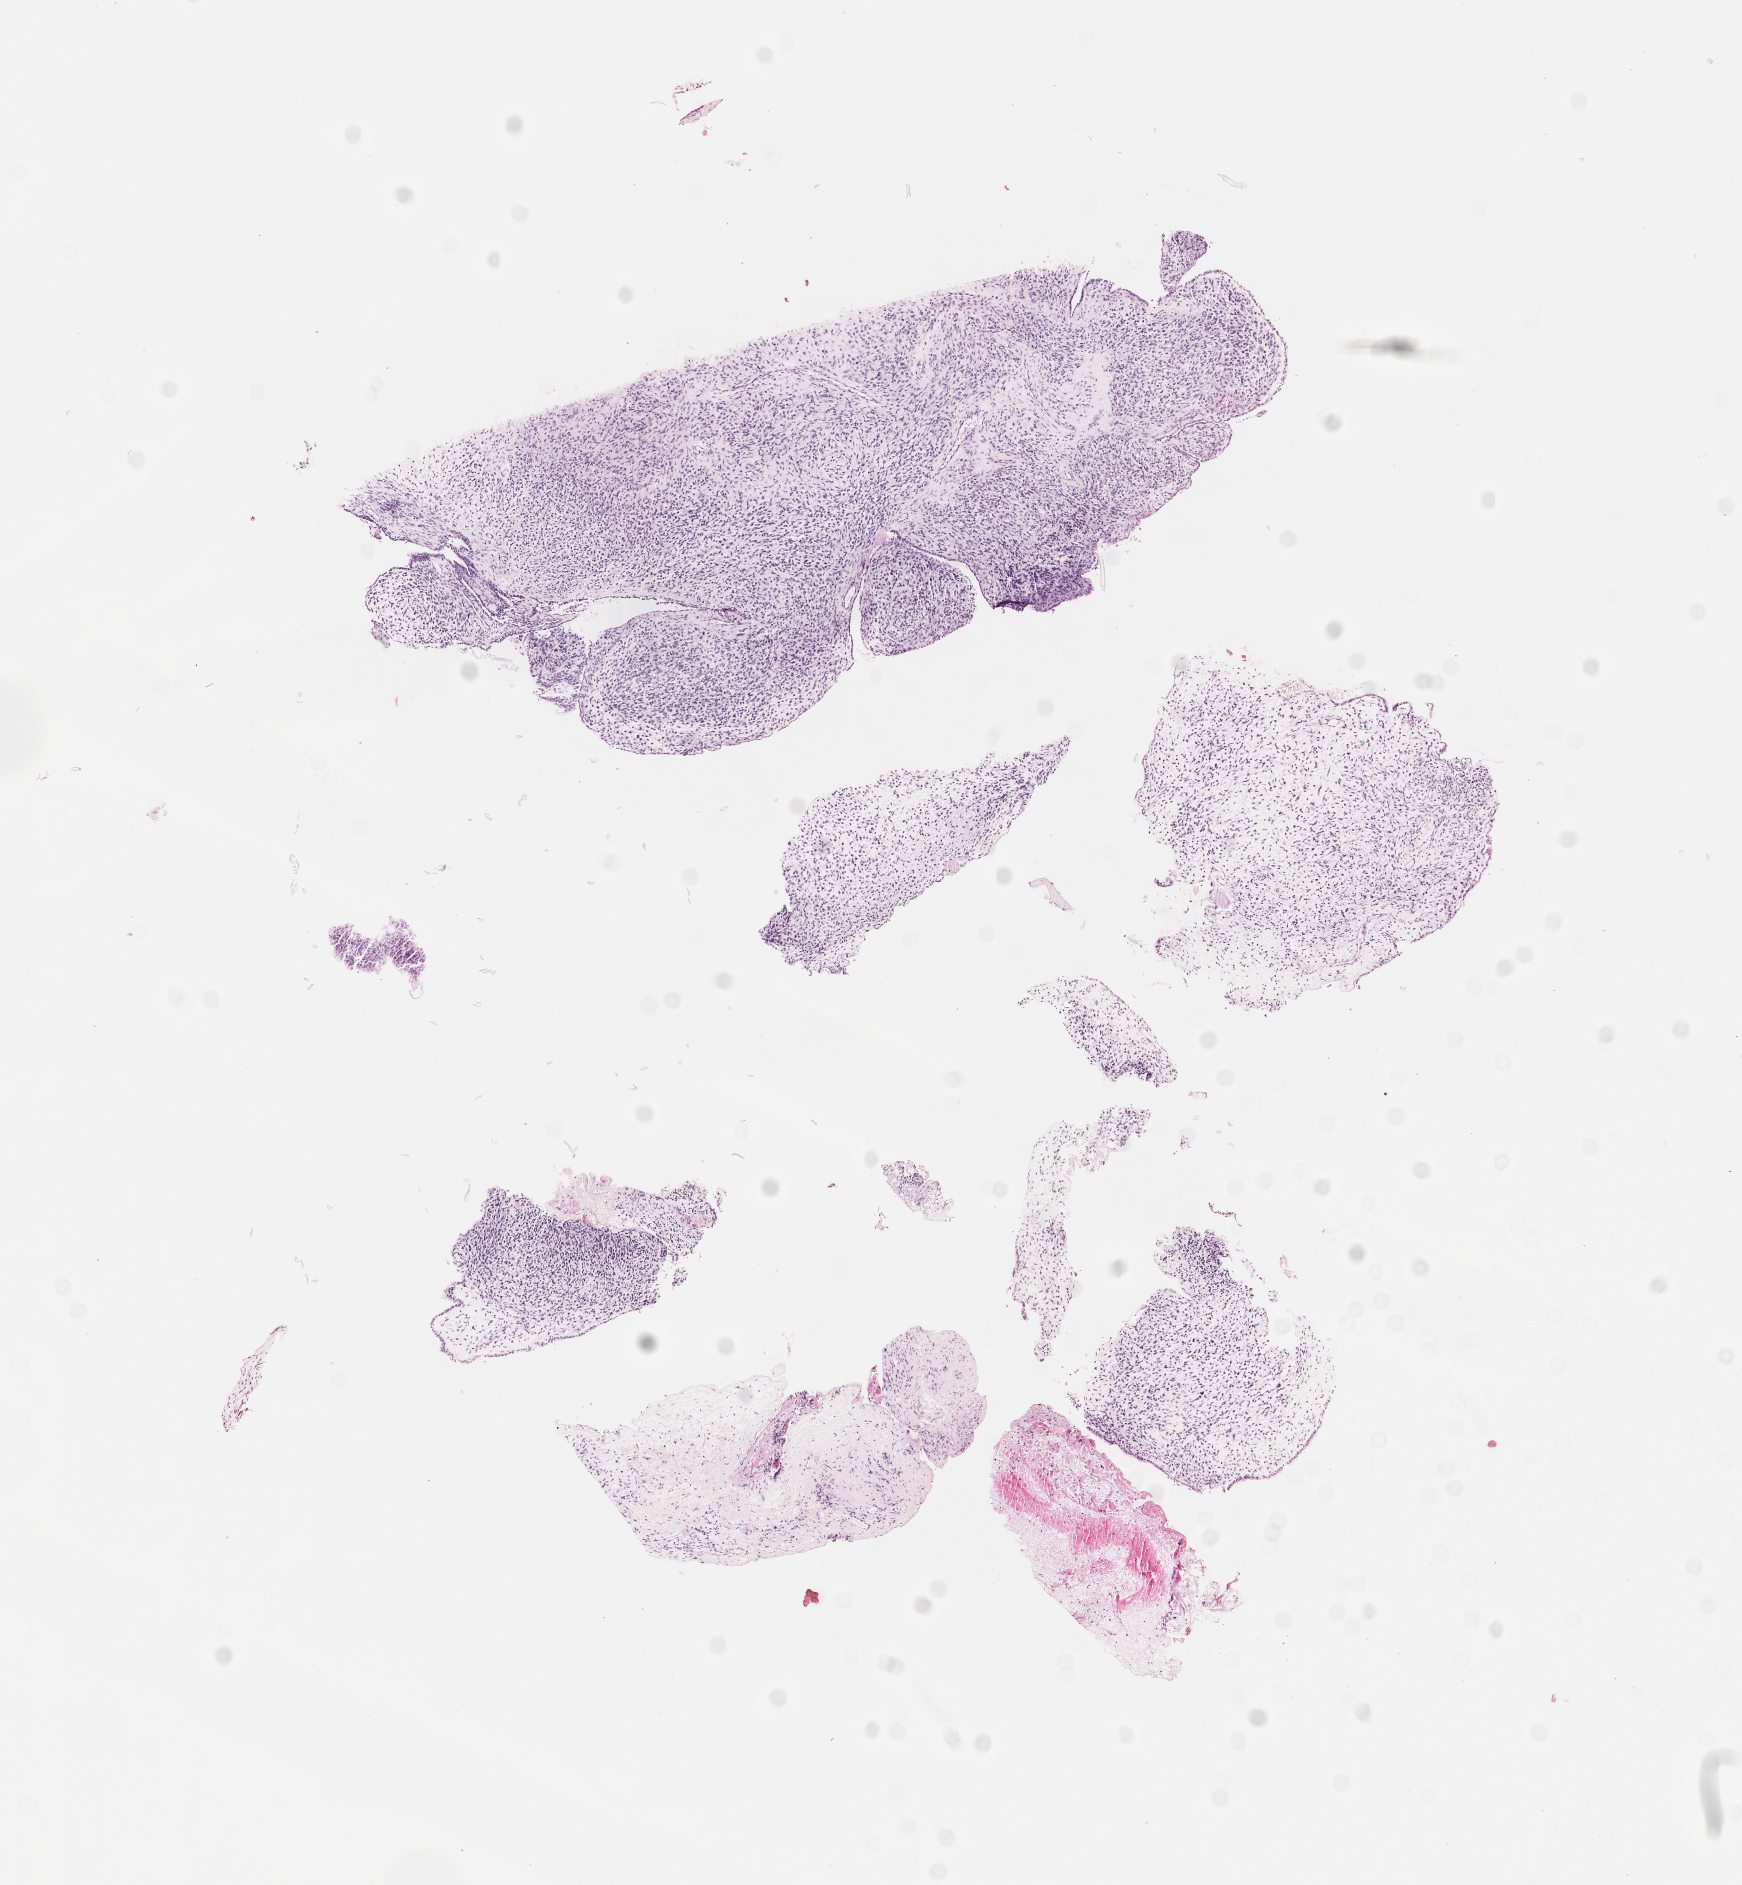
Hematoxylin and eosin (H&E) whole-slide image of tumor tissue — low-resolution overview of the scanned area, about 7.0 x 7.6 mm, formalin-fixed, paraffin-embedded (FFPE) tissue, sample anatomic site: soft tissue, ear-left (middle ear). Female patient, age at diagnosis 6.4 years.
Diagnosis: rhabdomyosarcoma; histological classification: embryonal rhabdomyosarcoma. Metastatic status at presentation (as recorded): non-metastatic. Stage (as recorded): 2.